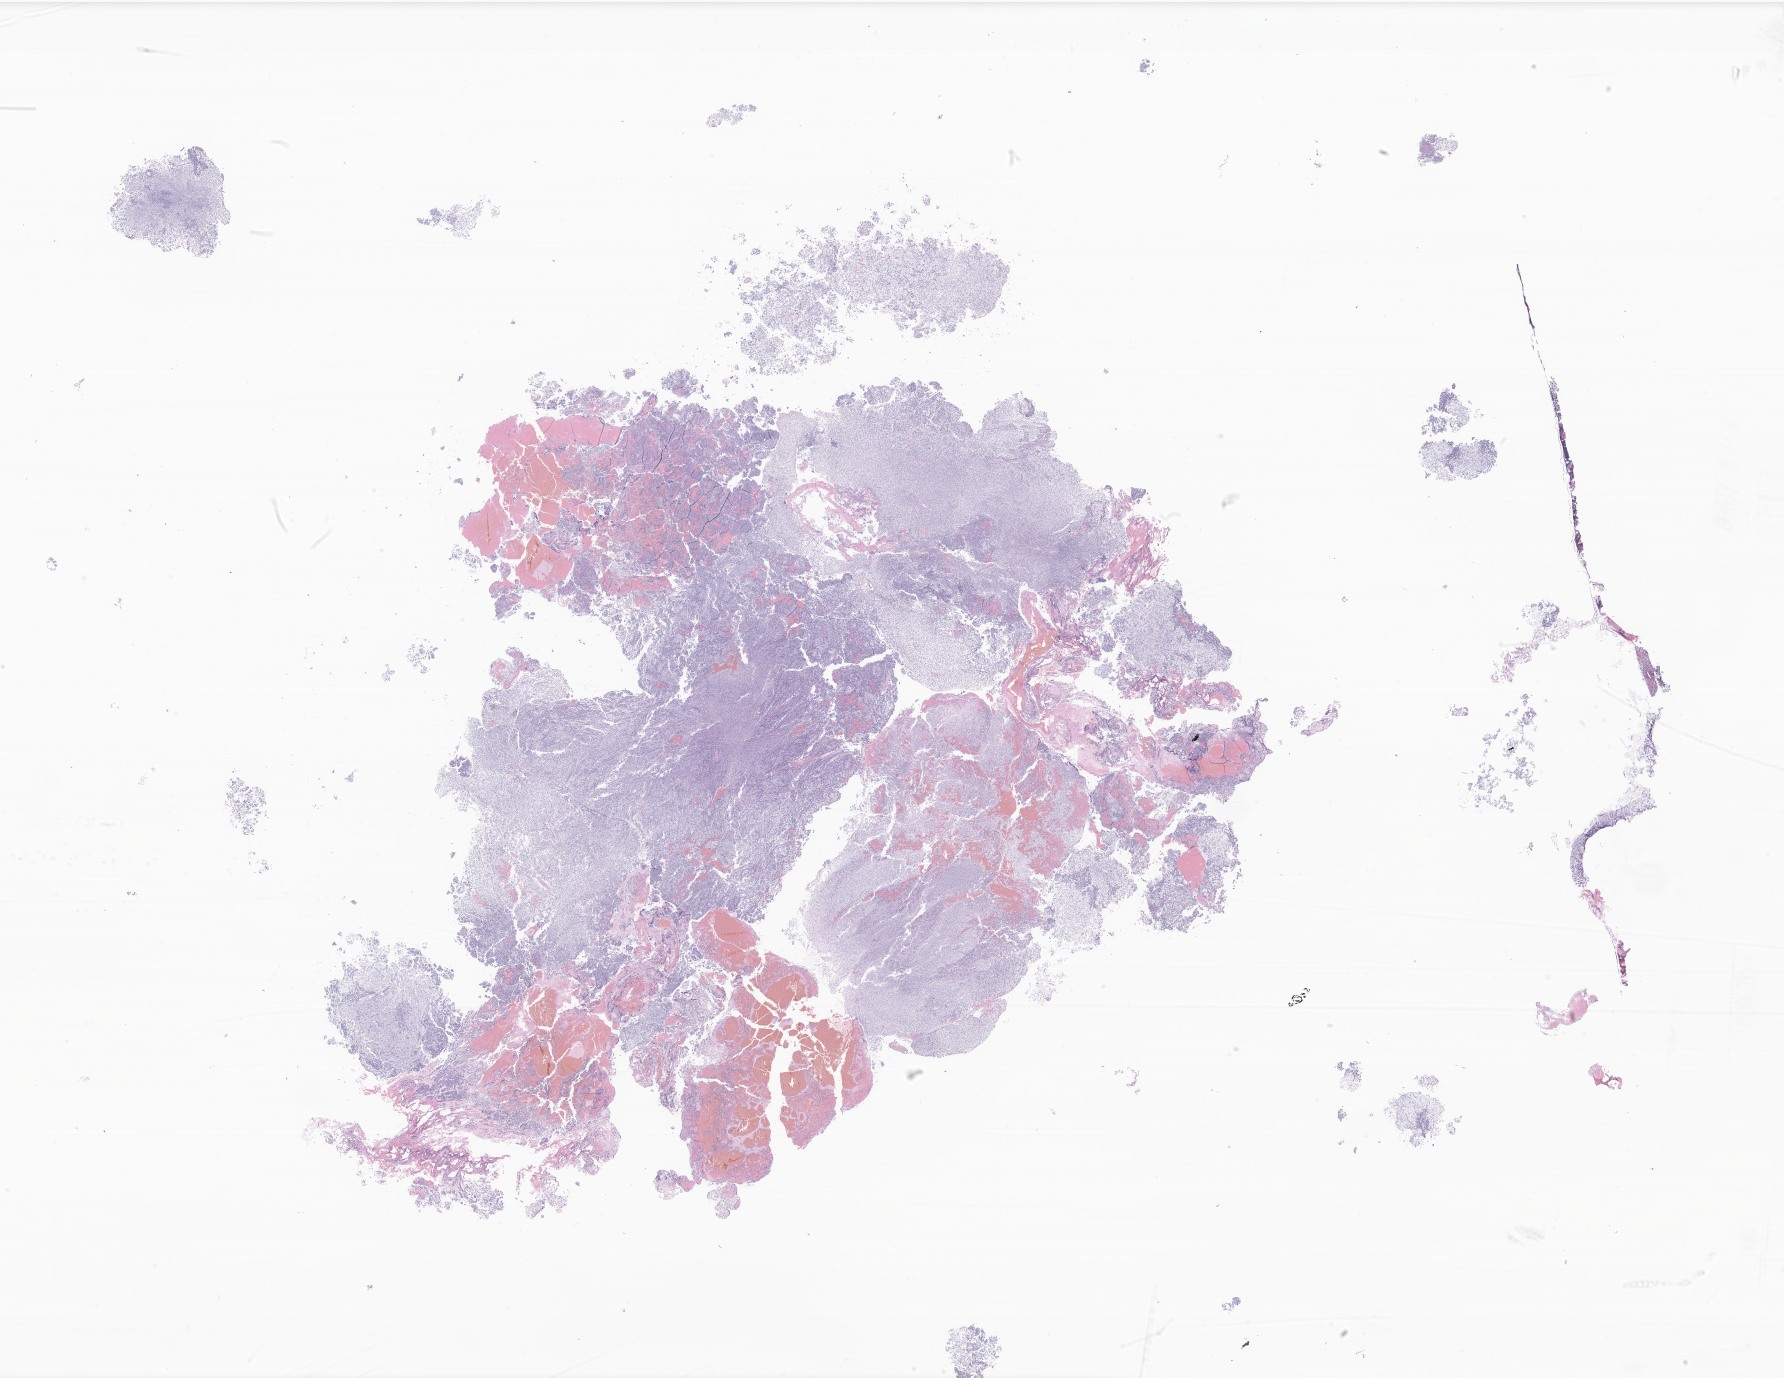
H&E whole-slide image of tumor tissue from the brain — whole scanned area (about 30.1 x 23.2 mm) shown as a low-resolution overview. Formalin-fixed paraffin-embedded section. Male patient, age 158 months.
Diagnosis (ICD-O-3 morphology term): Medulloblastoma, NOS.